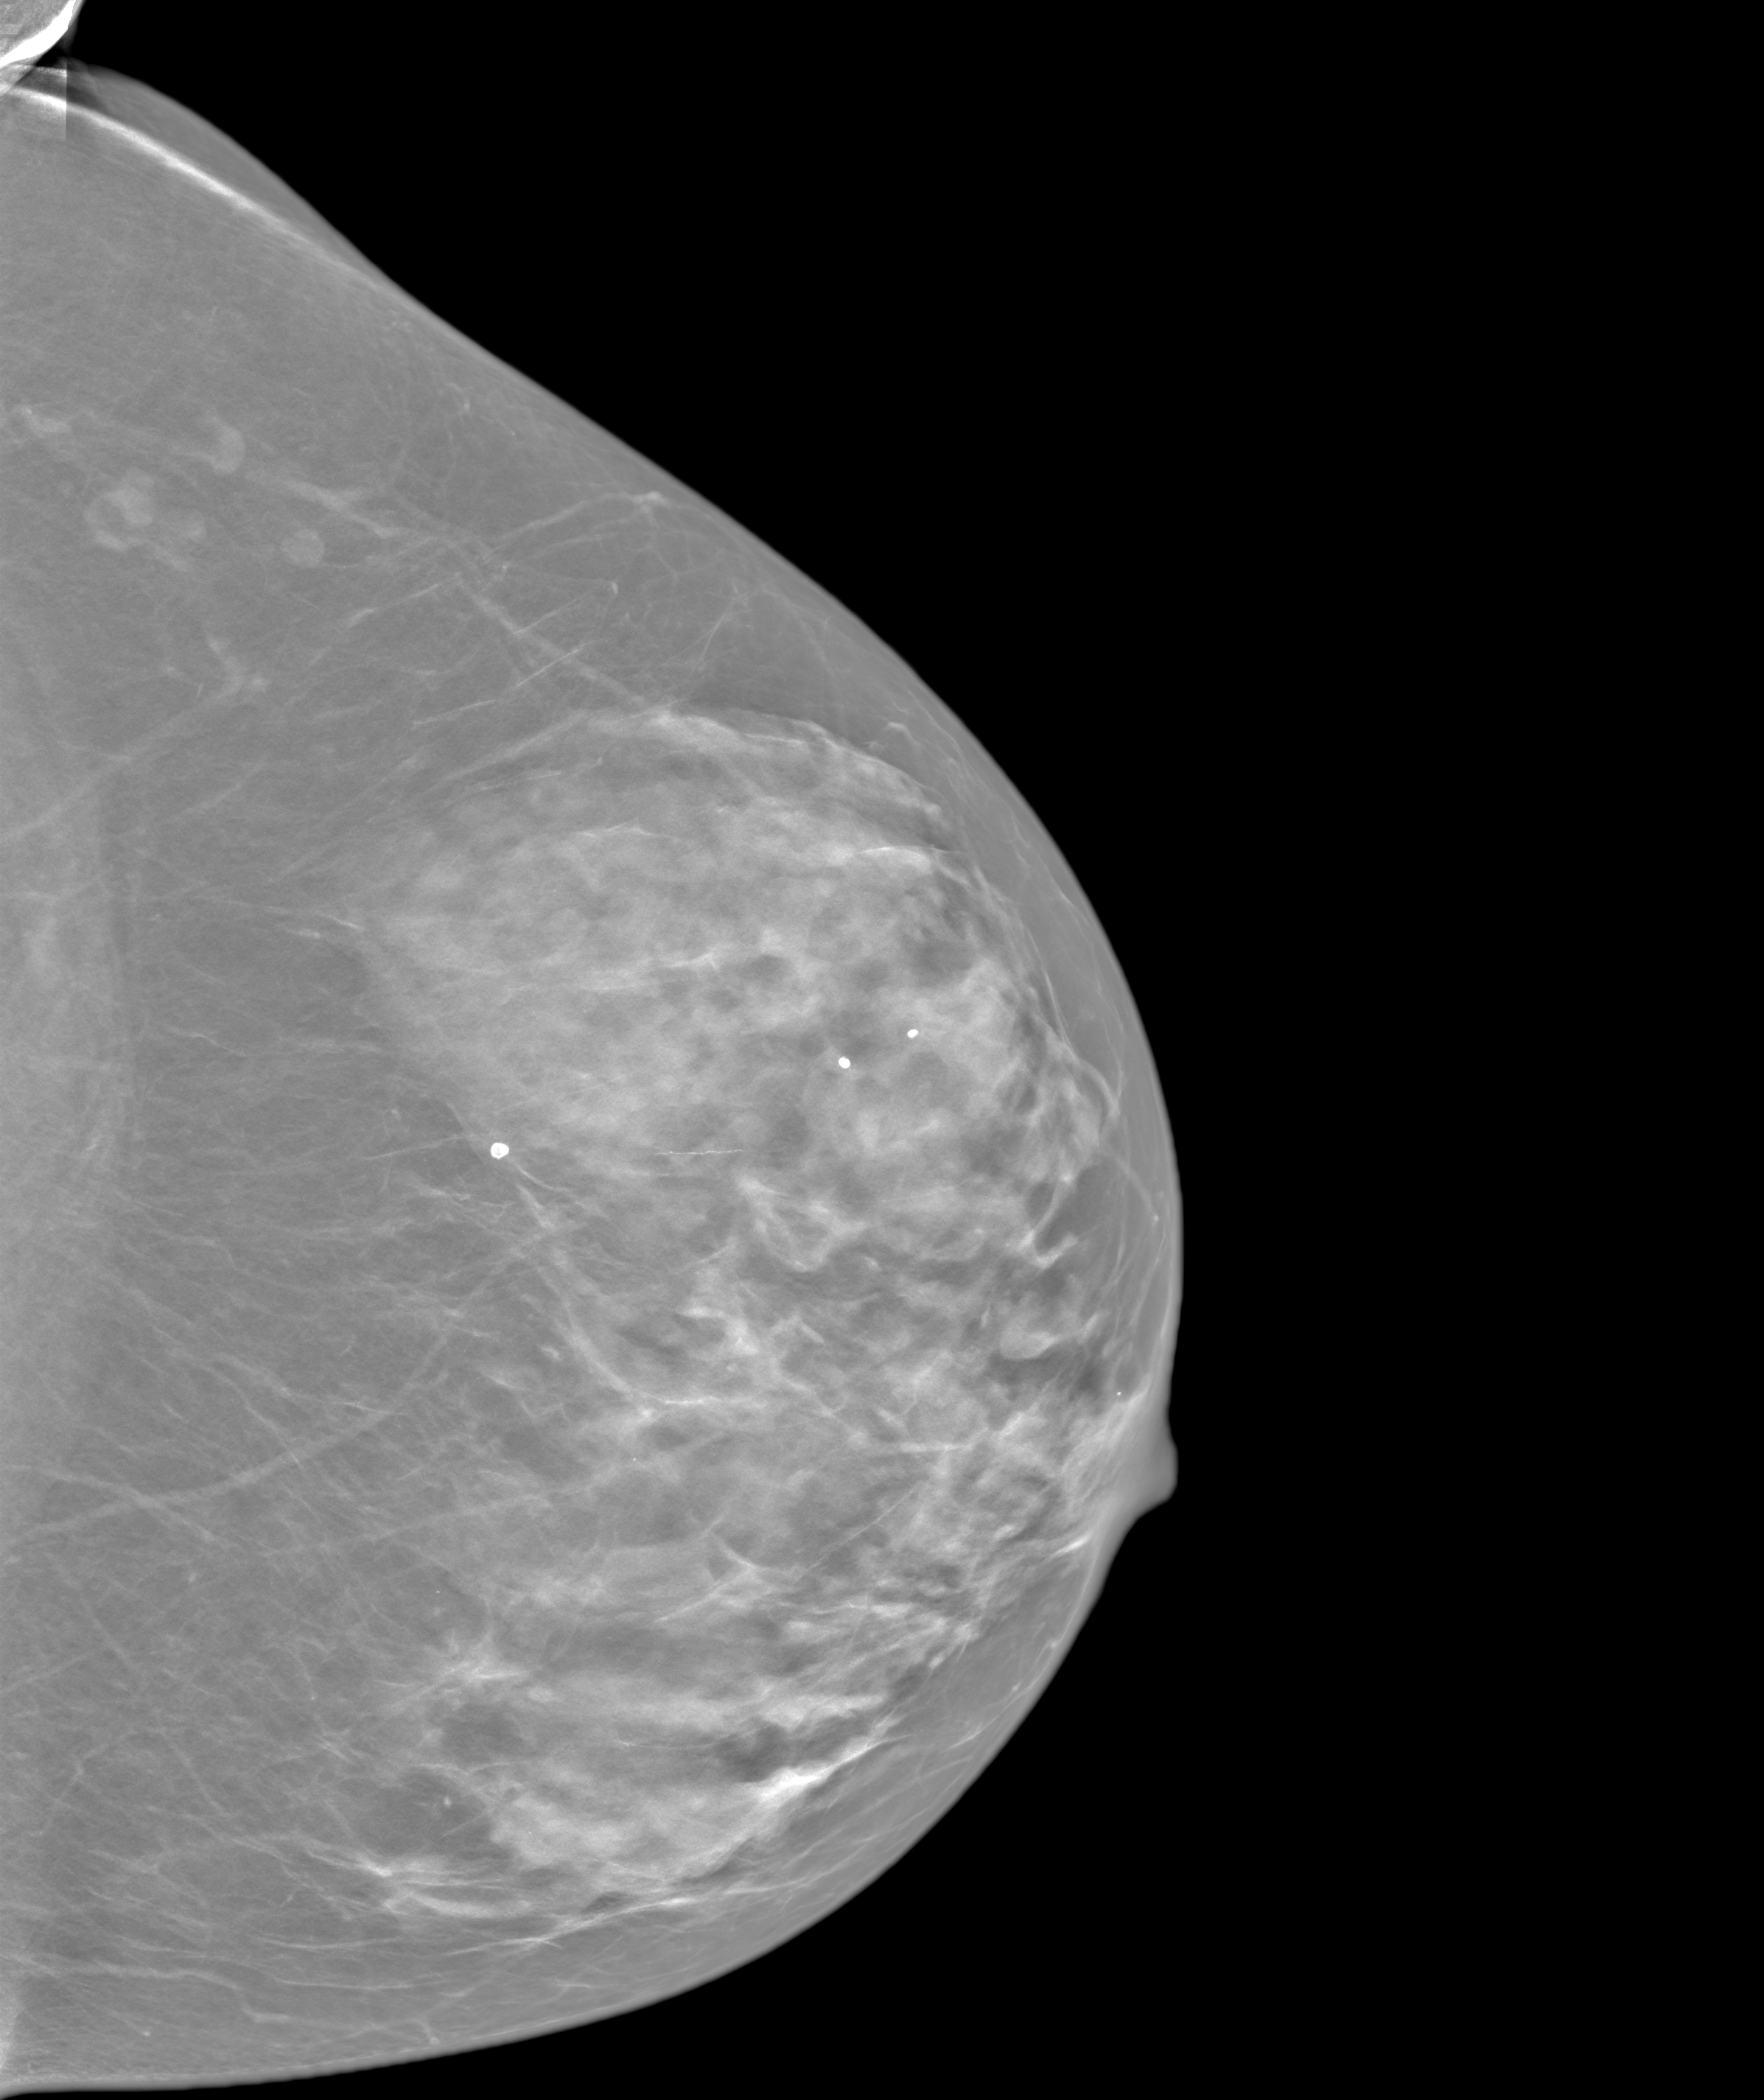
Screening examination; system: SenoIris_1SP2(440). Patient: female, 66 years.
Image type: synthesized 2-D view from tomosynthesis. Breast: left. Projection: CC view.